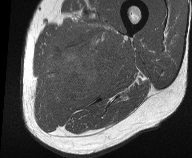
MRI of an extremity soft-tissue mass, one axial slice. Slice 16 of 61 in the series (ordered by position). MR volume resampled by the dataset authors to the PET/CT grid (not the native acquisition matrix). 192 × 158 image matrix. Male patient. From the clinical record (not read from this slice): histological type: pleiomorphic liposarcoma; grade: high; site of the primary tumour: left thigh.
Outlined on this slice (expert contour drawn on MRI and transferred to this co-registered scan by the dataset authors):
- gross tumour volume including surrounding oedema: bounding box [x1, y1, x2, y2] px = [48, 18, 122, 99]
- gross tumour volume (mass): [54, 50, 104, 95]